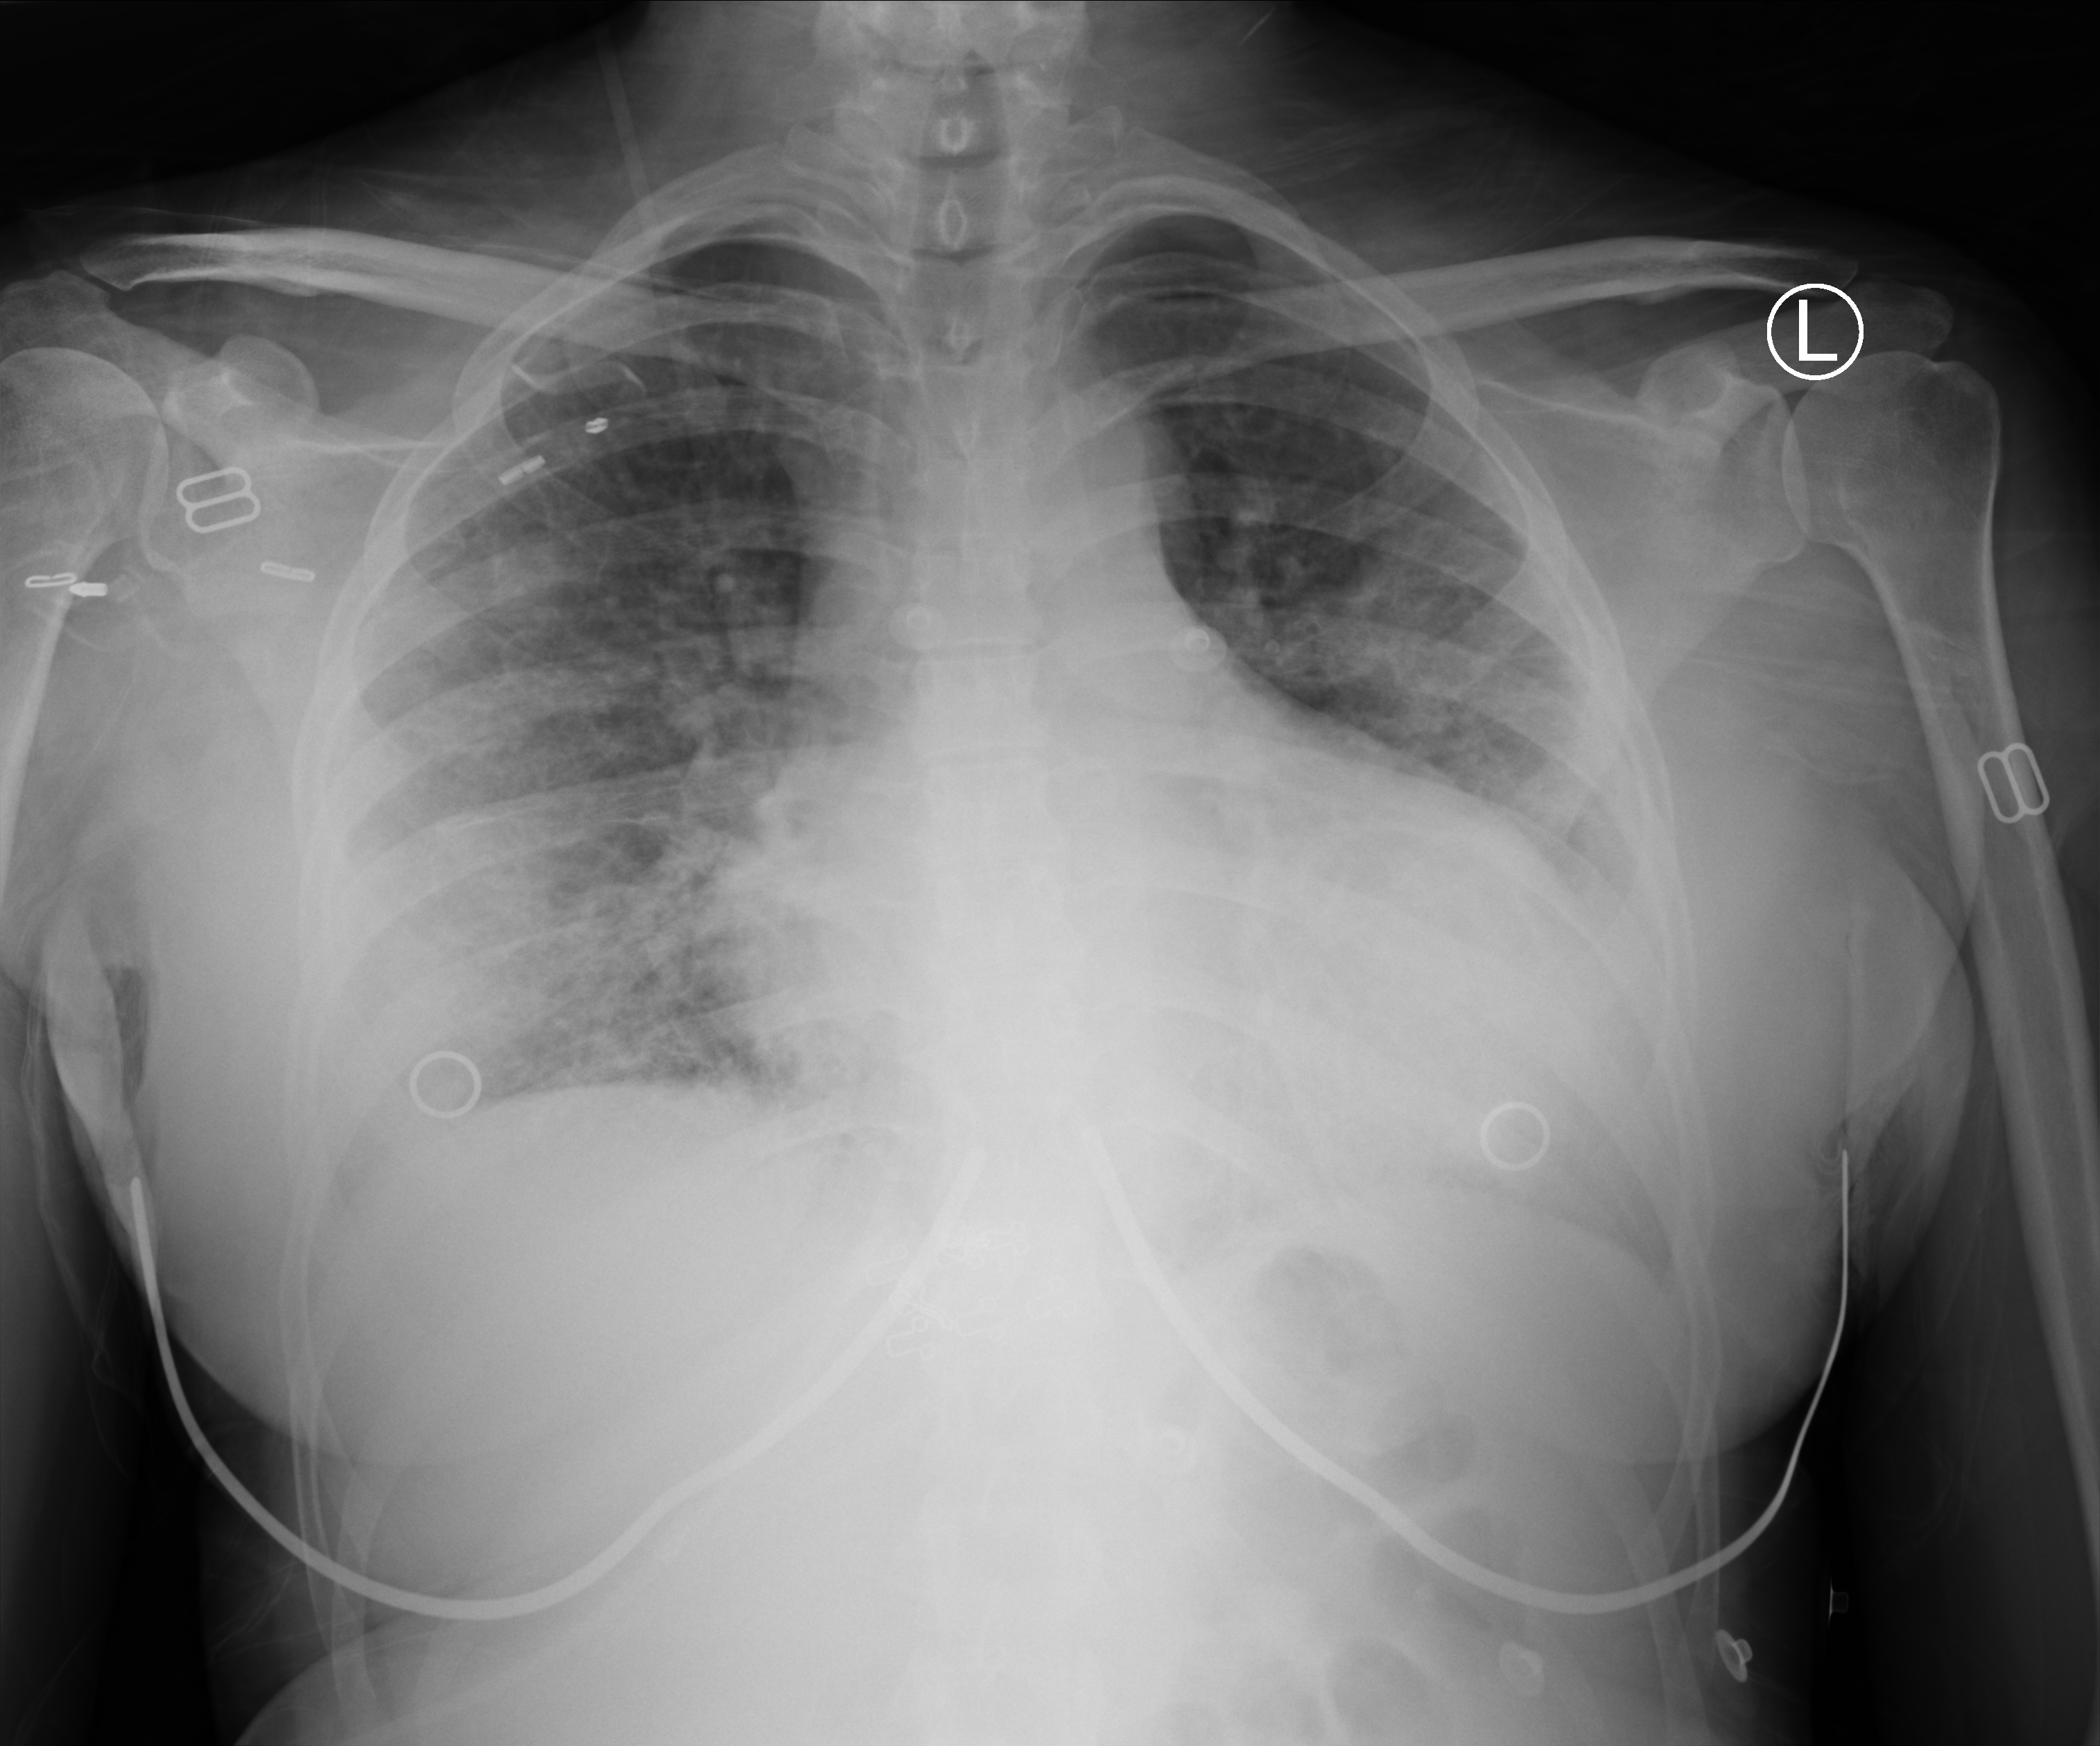
Chest X-ray (portable). Female patient hospitalised with COVID-19, age 18–59 years.
Hospital-stay facts (about this admission, not read from this image; timing relative to this image not recorded): admitted to intensive care during this hospital stay: no.